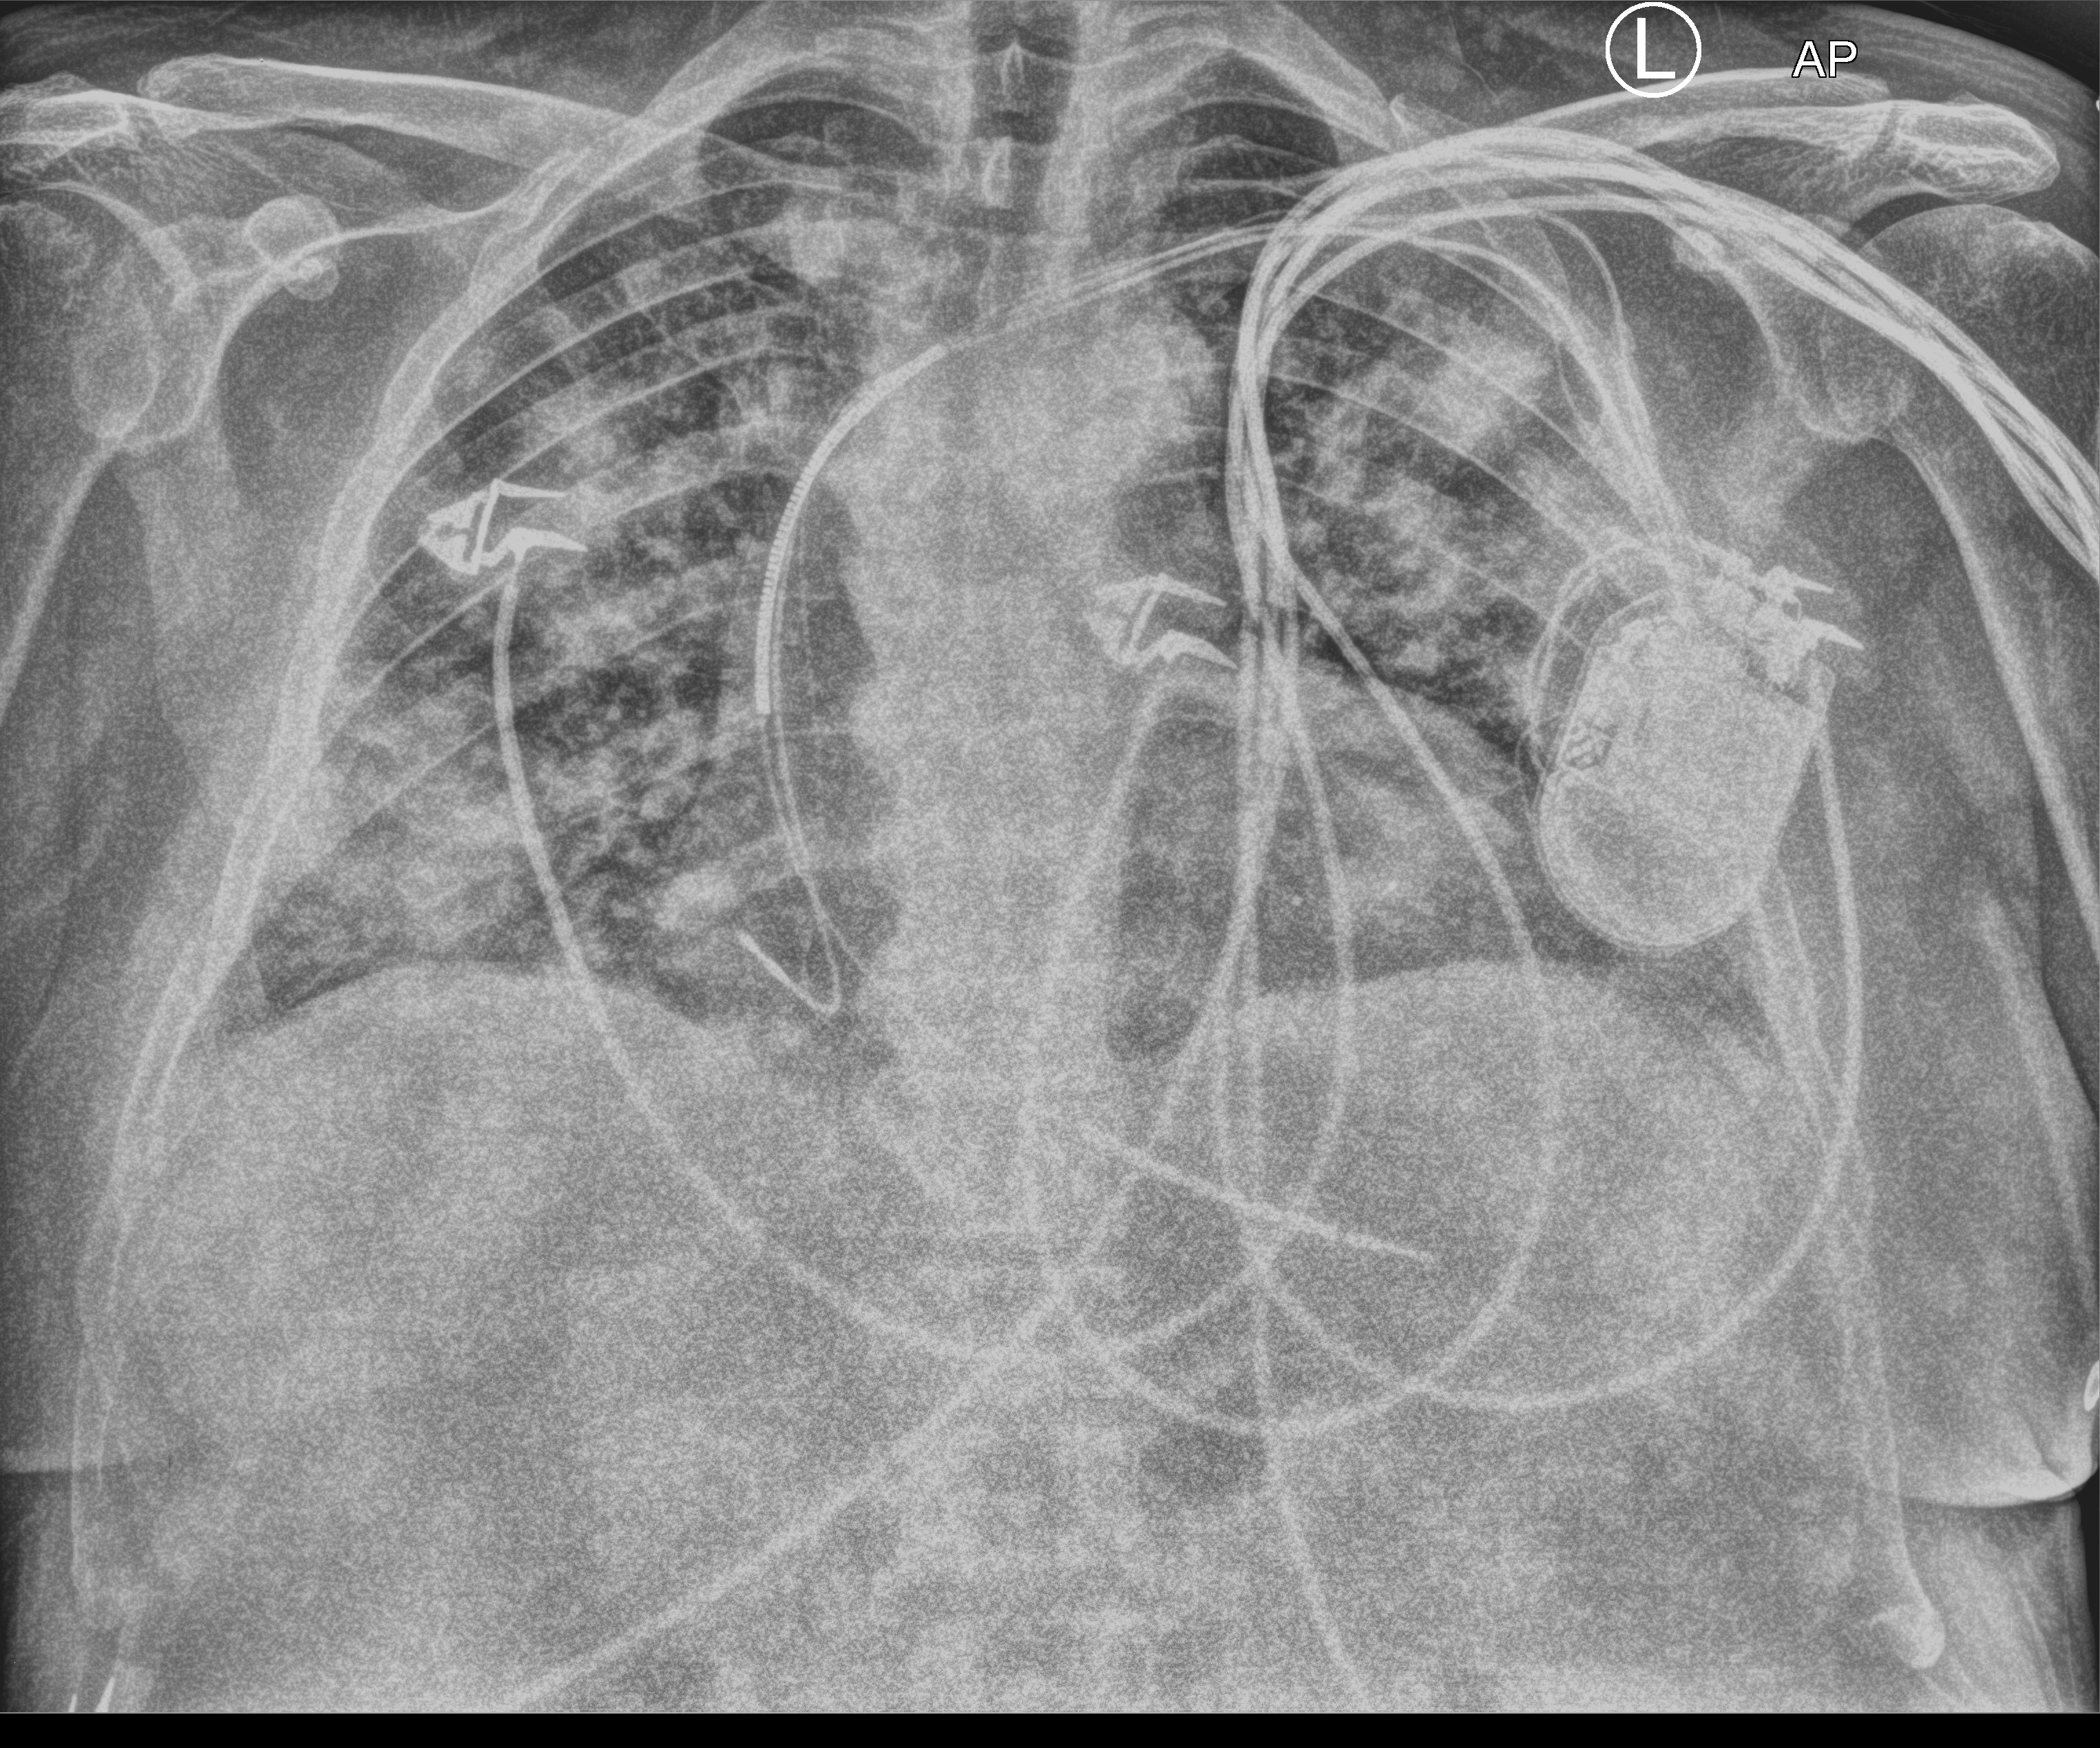
Bedside chest radiograph (computed radiography), anteroposterior (AP) projection. Male patient hospitalised with COVID-19, age 60–74 years.
From the hospital-stay record, not from the radiograph (when in the stay this image was taken is not recorded): chronic kidney disease (admission record): no.